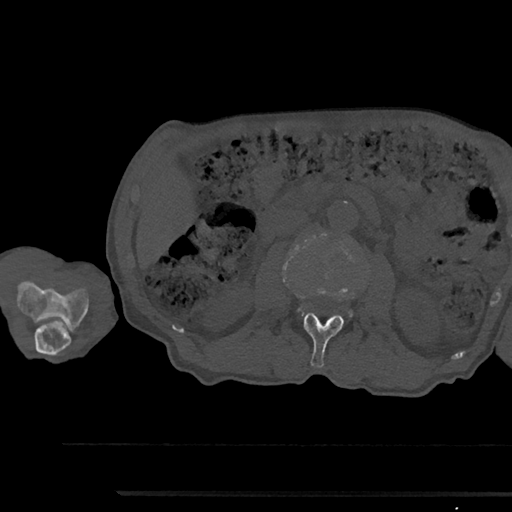
CT including the spine, one axial slice. Position 536 of 797 along the scan axis. 120 kVp. Bone window (W 1800 / L 400 HU). 512 × 512 image matrix, field of view 367 × 367 mm. Male patient, age 79 years. From the clinical record (not read from this slice): primary cancer: prostate.
Outlined on this slice (semi-automatically segmented with operator editing):
- L2 vertebra: box from (x=304, y=312) to (x=344, y=367) px
- L3 vertebra: (x=299, y=308)–(x=352, y=315)